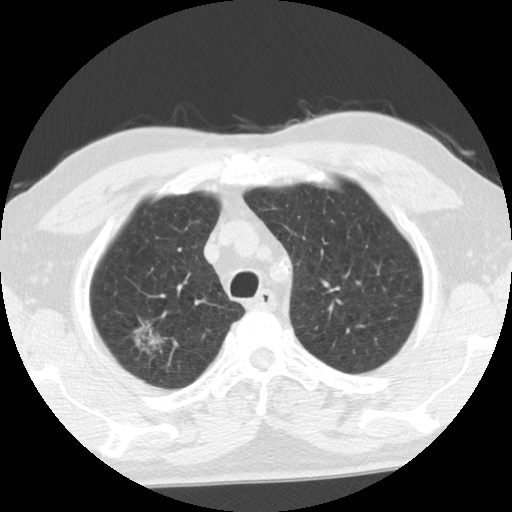
Chest CT (low-dose screening protocol), one axial image. Second annual screen. Lung window (W 1500 / L -600 HU). 2.5 mm slice thickness. 140 kVp. Slice 92 of 116 in the series. 512 × 512 image matrix, field of view 330 × 330 mm. Male participant, aged 68 years at enrolment.
• Expert reader's lesion annotation, bounding box <129,314,166,351> (left, top, right, bottom; pixels).
• The exam's reader record, not a measurement of the box and not confirmed to be the same lesion: non-calcified nodule or mass ≥4 mm, right upper lobe, poorly defined margins, ground glass attenuation, pre-existing on the prior screen: yes; interval growth: yes.
• Later outcome: lung cancer diagnosed 88 days after this screen — adenocarcinoma, NOS, right upper lobe, moderately differentiated (G2), stage IA (AJCC 6th edition), 28 mm at pathology.